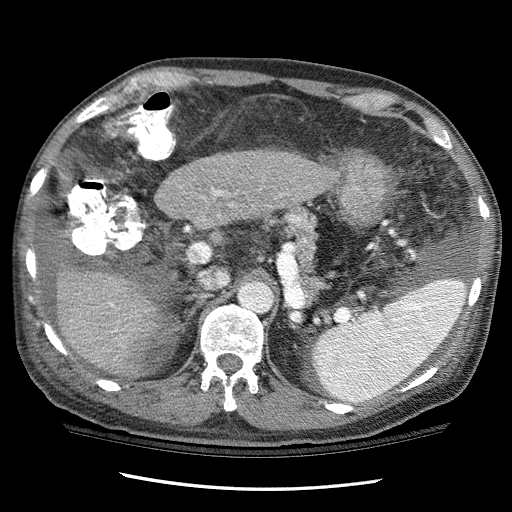
Contrast-enhanced abdominal CT (liver protocol), one axial slice; position 64 of 114 along the scan axis; one of 3 acquisitions stored at this slice position; soft-tissue window (W 400 / L 40 HU); 2.5 mm slice thickness; 512 × 512 image matrix, field of view 360 × 360 mm. From the clinical record (not read from this slice): diagnosis: hepatocellular carcinoma (patient treated with transarterial chemoembolisation; whether this scan precedes or follows treatment is not stated here); TNM stage (as recorded): Stage-I; Child-Pugh class: C; tumour differentiation: well differentiated; tumour nodularity: uninodular.
Annotated regions visible in this slice (semi-automatic segmentation, software-assisted and operator-edited):
- liver parenchyma outside the tumour (the mass and vessels are separate outlines, so this box may not span the whole liver): bounding box [x1, y1, x2, y2] px = [56, 148, 339, 376]
- liver vessels: [109, 191, 222, 306]